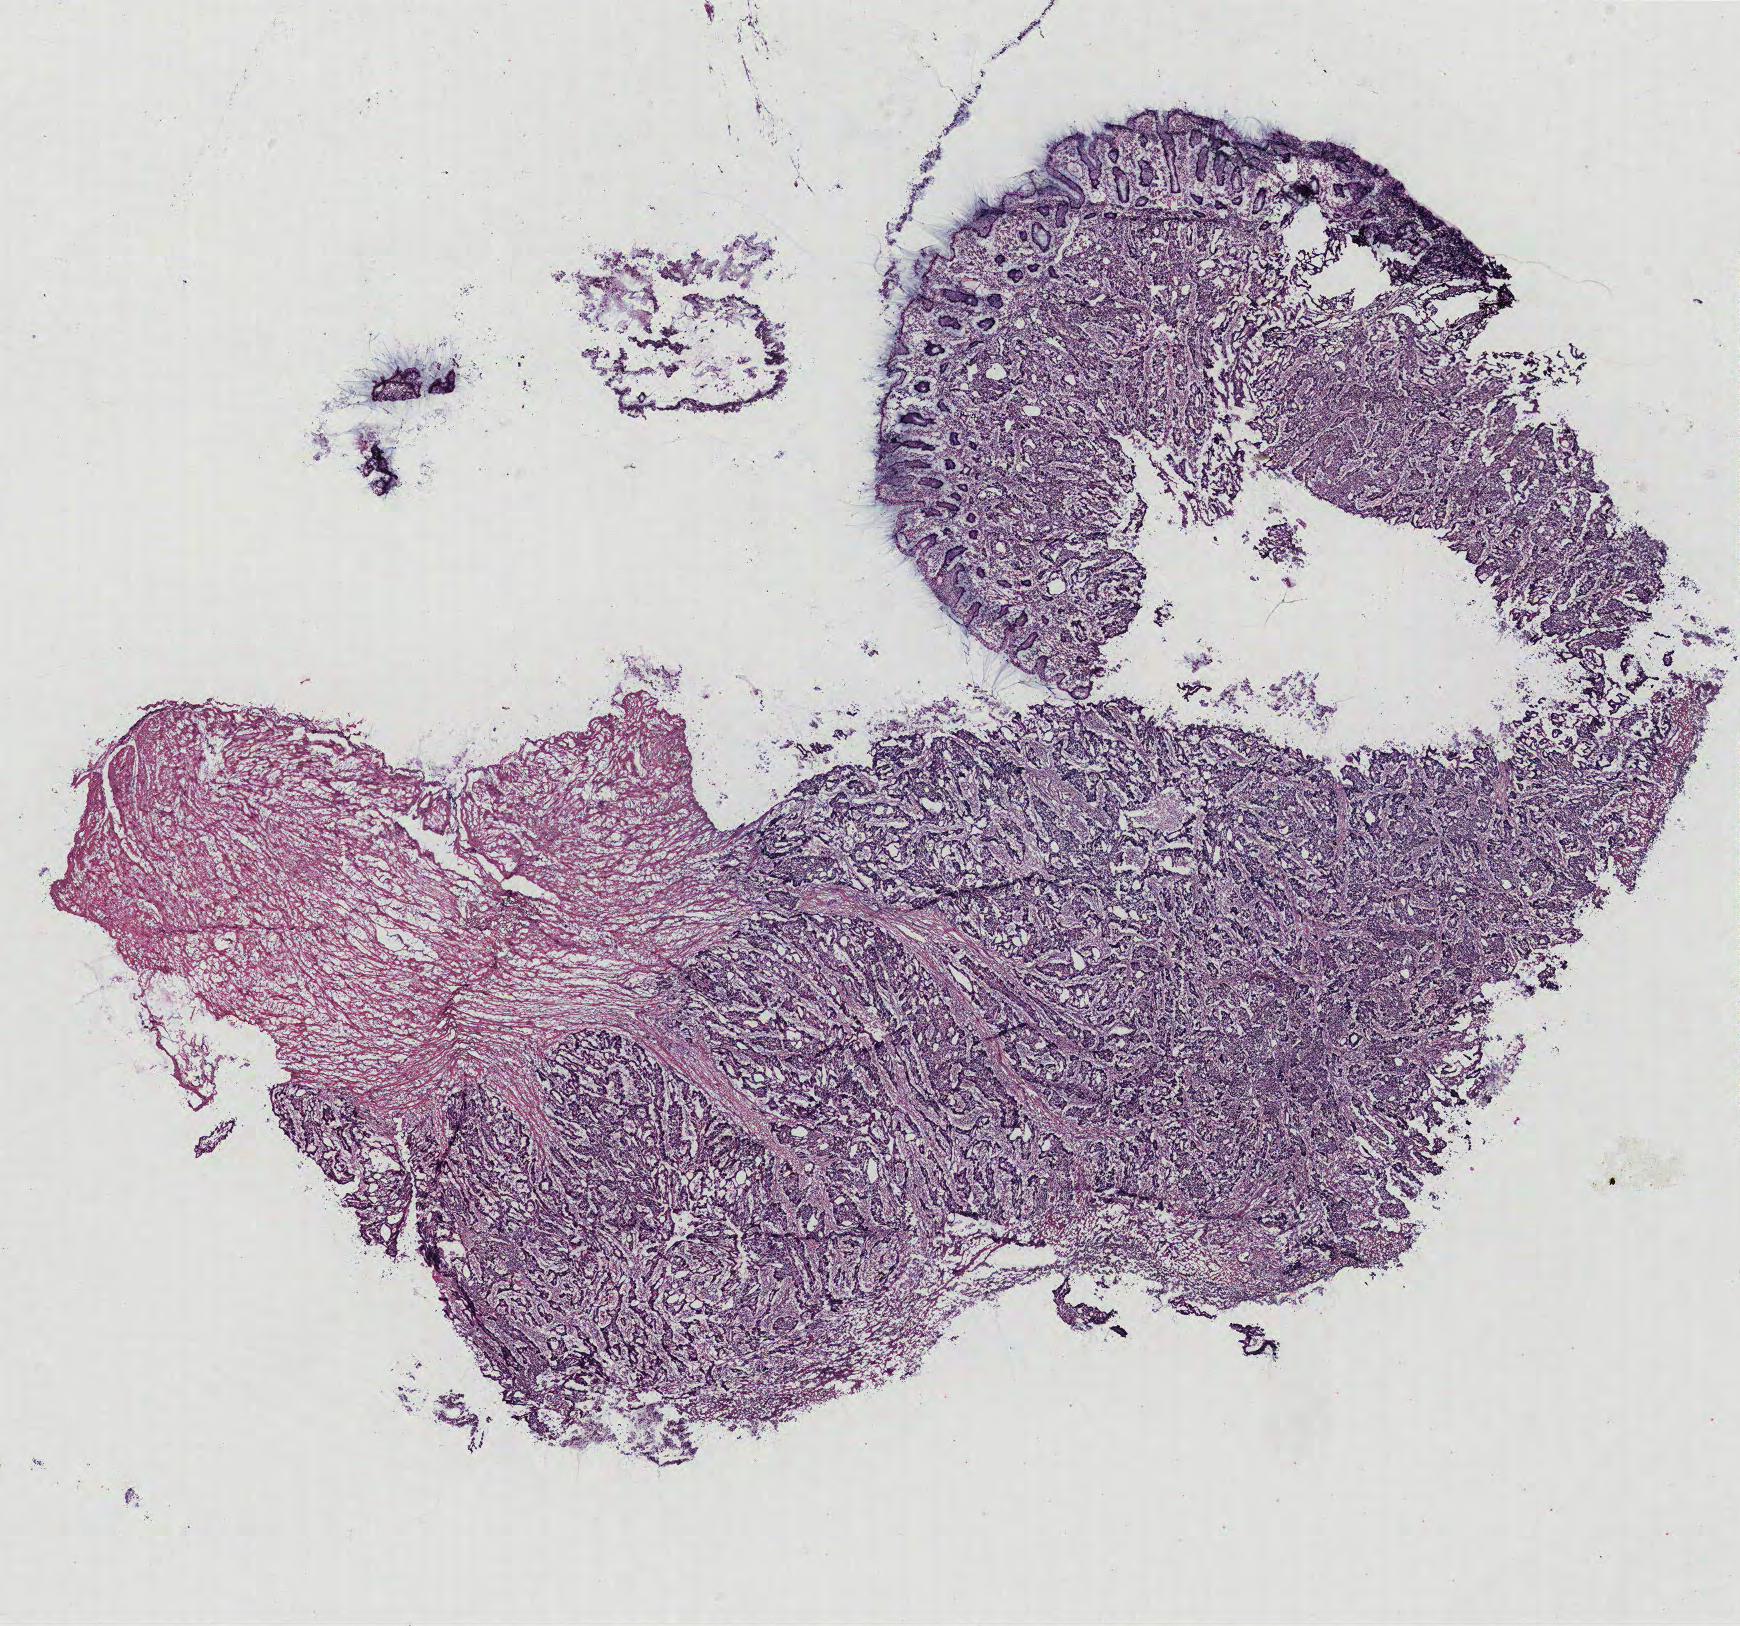
Whole-slide histology image, H&E-stained, a low-resolution overview of the entire scanned area, about 13.9 x 13.0 mm (slide scanned at 40x), tumour tissue sample, colon. Male, 57 y/o.
Histologic diagnosis: Adenocarcinoma, NOS.